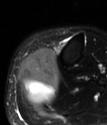
MRI of an extremity soft-tissue mass, one axial slice; position 25 of 78 along the scan axis; T2-weighted fat-saturated; MR volume resampled by the dataset authors to the PET/CT grid (not the native acquisition matrix); 3.27 mm slice thickness; 107 × 125 image matrix, field of view 104 × 122 mm. Female patient. Case-level facts recorded for this patient, not image findings: histological type: extraskeletal high grade osteogenic sarcoma; grade: high; site of the primary tumour: left calf.
Structures marked on this image (expert contour drawn on MRI and transferred to this co-registered scan by the dataset authors):
- gross tumour volume (mass): box from (x=19, y=49) to (x=59, y=105) px